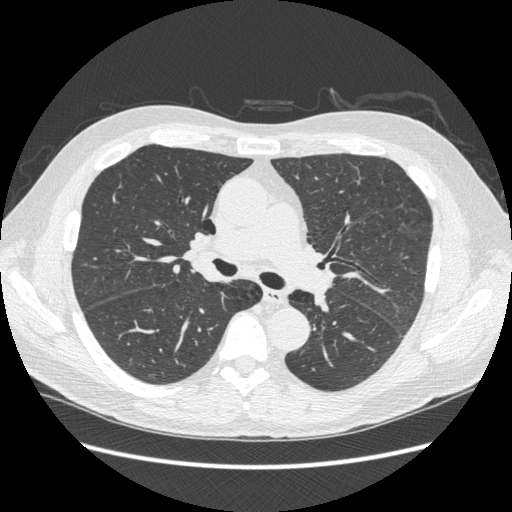
Chest CT (low-dose screening protocol), one axial image. Third annual screen. Lung window (W 1500 / L -600 HU). 1.25 mm slice thickness. Slice 109 of 258 in the series. Male participant, aged 59 years at enrolment.
- Expert reader's lesion annotation, bounding box <180,225,232,266> (left, top, right, bottom; pixels).
- The screening reader recorded 2 non-calcified nodules or masses ≥4 mm on this exam (right upper lobe, left lower lobe); which of them this box marks is not recorded.
- Official screen result: negative screen, minor abnormalities not suspicious for lung cancer.
- Participant outcome: lung cancer diagnosed 169 days after this screen — squamous cell carcinoma, keratinizing, NOS, right hilum, stage IIIB (AJCC 6th edition).